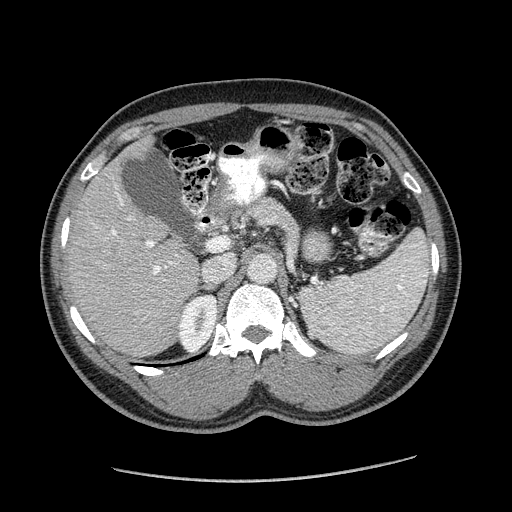
Contrast-enhanced abdominal CT (liver protocol), one axial slice; slice 107 of 182 in the series (ordered by position); reconstruction kernel STANDARD; 120 kVp; soft-tissue window (W 400 / L 40 HU); 2.5 mm slice thickness; 512 × 512 image matrix. From the clinical record (not read from this slice): diagnosis: hepatocellular carcinoma (patient treated with transarterial chemoembolisation; whether this scan precedes or follows treatment is not stated here); TNM stage (as recorded): Stage-I; Child-Pugh class: A; tumour differentiation: well differentiated; tumour size: 3.1 cm.
Annotated regions visible in this slice (semi-automatically segmented with operator editing):
- liver parenchyma outside the tumour (the mass and vessels are separate outlines, so this box may not span the whole liver): bounding box (x1, y1, x2, y2) in pixels: (66, 136, 200, 356)
- mass: (89, 238, 127, 267)
- liver vessels: (112, 187, 177, 275)